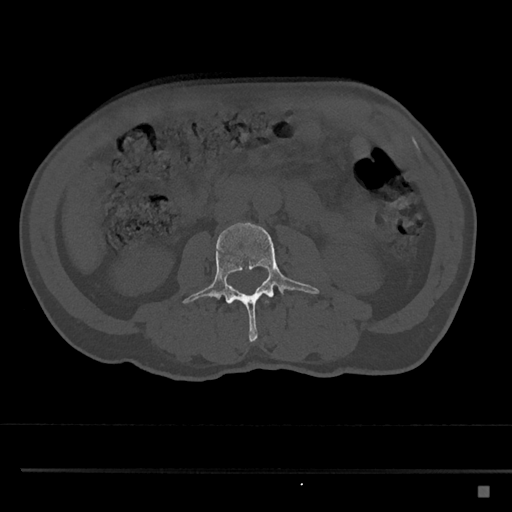
CT including the spine, one axial slice; position 699 of 797 along the scan axis; 120 kVp; bone window (W 1800 / L 400 HU); 512 × 512 image matrix, field of view 391 × 391 mm. Male patient, age 59 years. From the clinical record (not read from this slice): primary cancer: prostate.
Annotated regions visible in this slice (semi-automatic segmentation, software-assisted and operator-edited):
- L2 vertebra: bounding box <227,301,268,304> (left, top, right, bottom; pixels)
- L3 vertebra: <183,222,320,343>